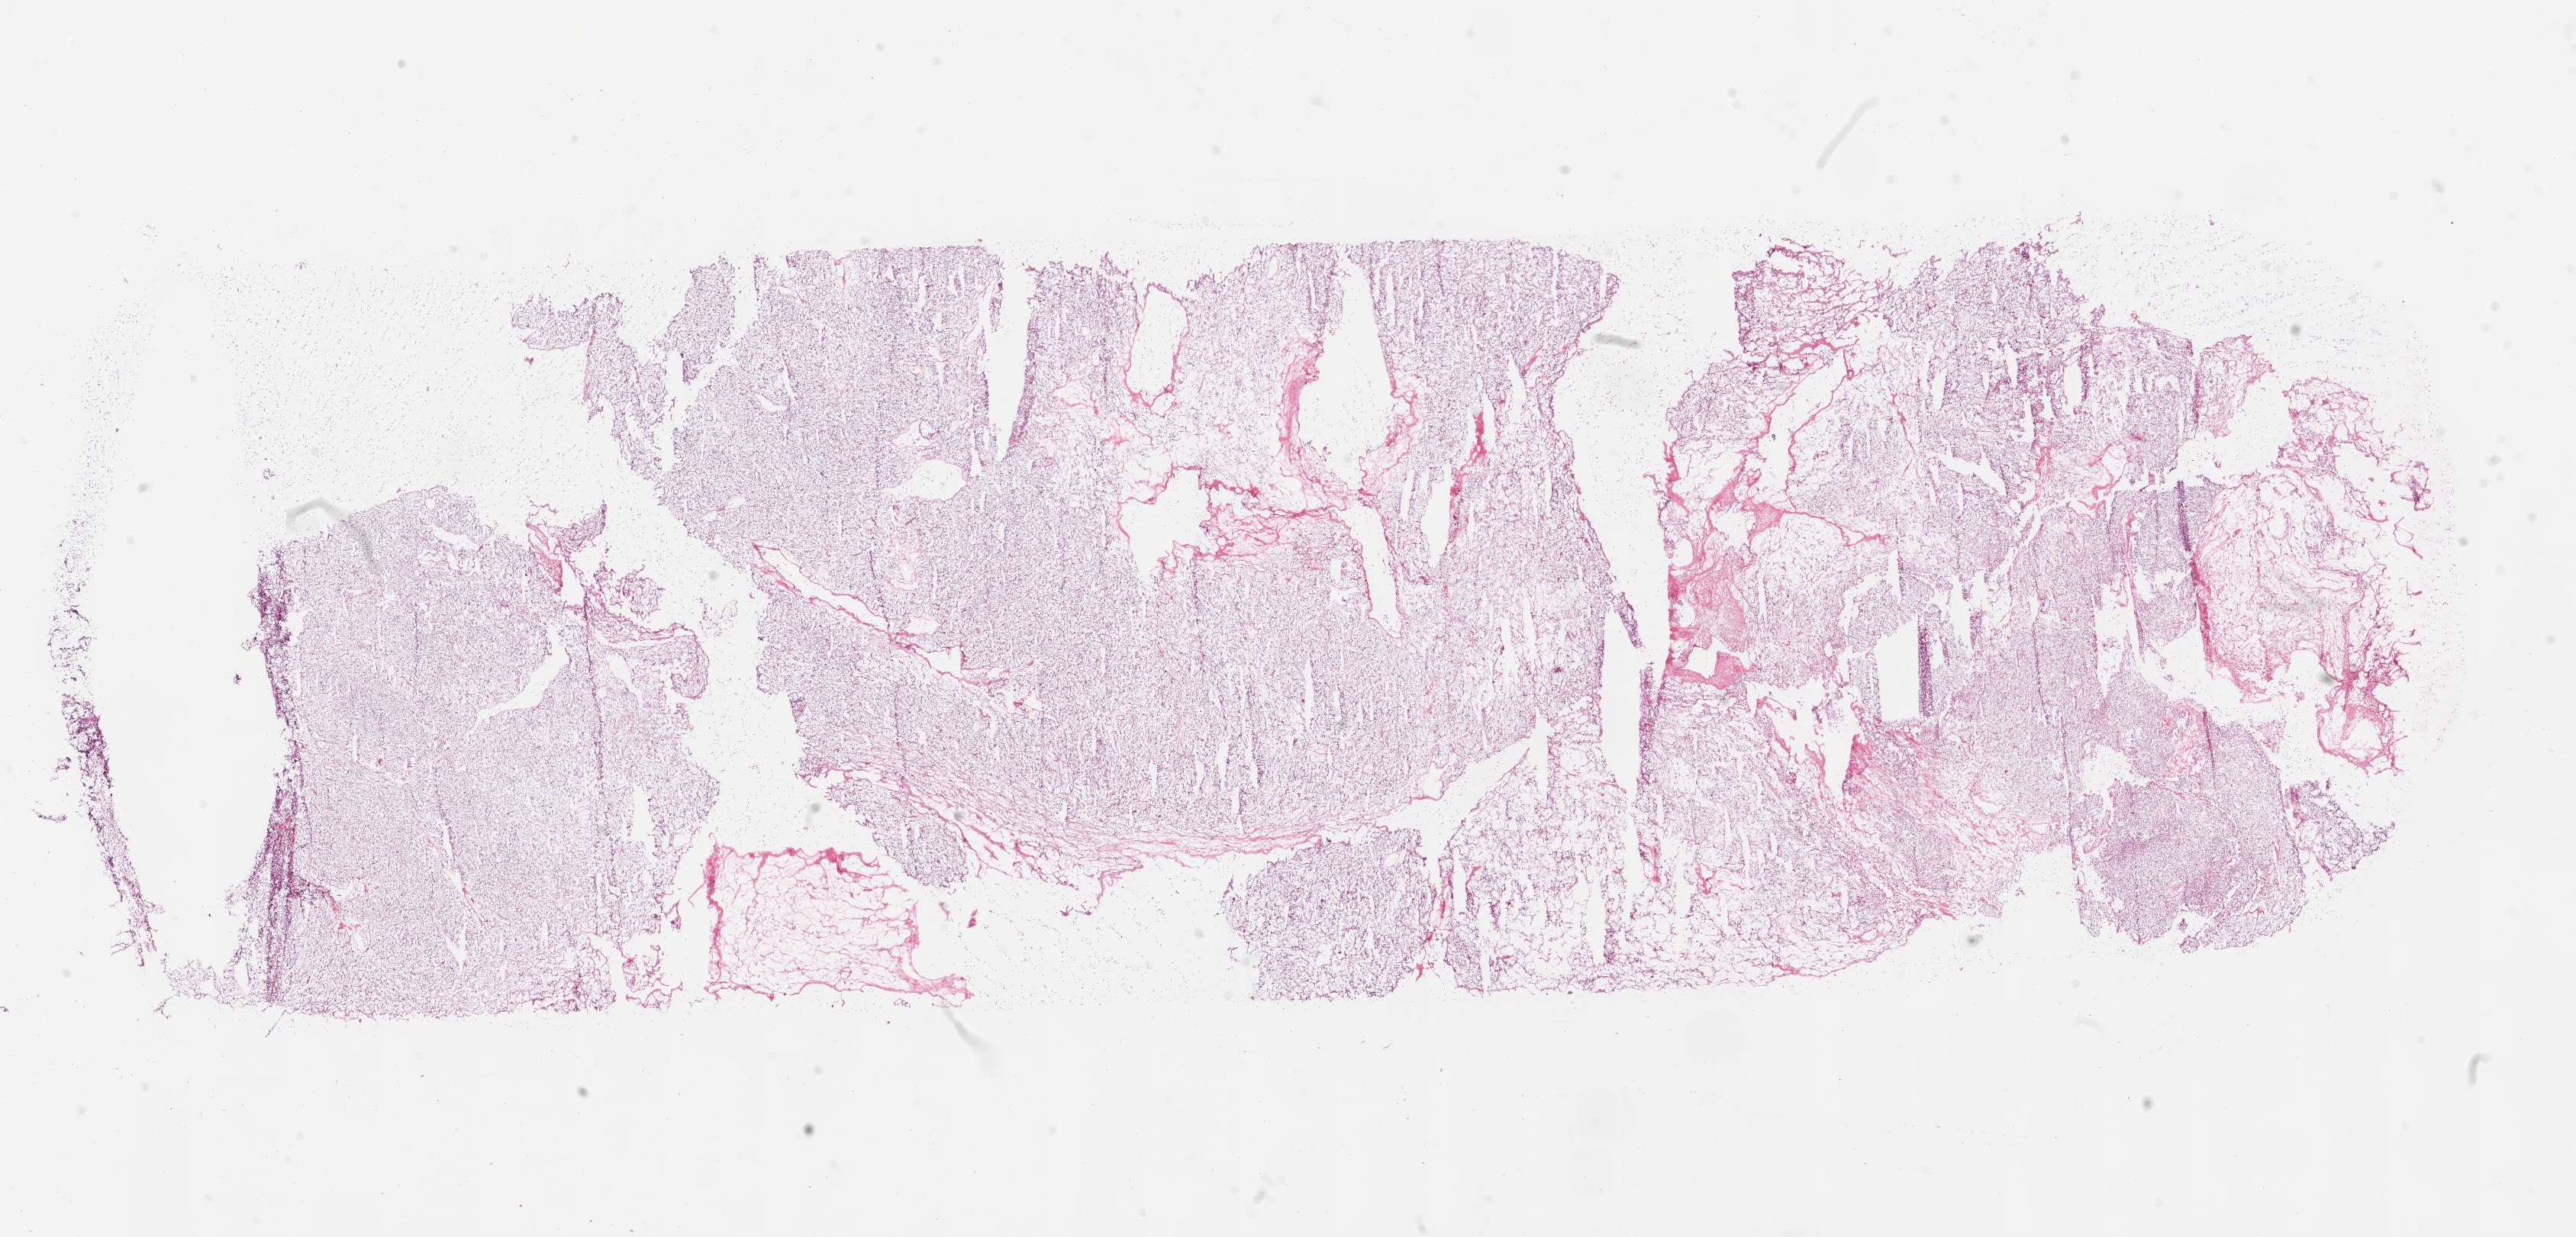
H&E-stained whole-slide image, shown as a low-resolution overview of the whole scanned area (about 27.1 x 13.0 mm, acquisition: 20x scan). Frozen section. Kidney, primary tumour sample. Patient: female, age at initial diagnosis 49 years. Histologic grade: G2 (moderately differentiated). Composition of this section per pathologist review: tumour cells 95%, tumour nuclei 80%, normal cells 0%, stromal cells 5%, necrosis 0%.
AJCC pathologic stage: II. Histologic diagnosis: Clear cell adenocarcinoma, NOS. Laterality: left.